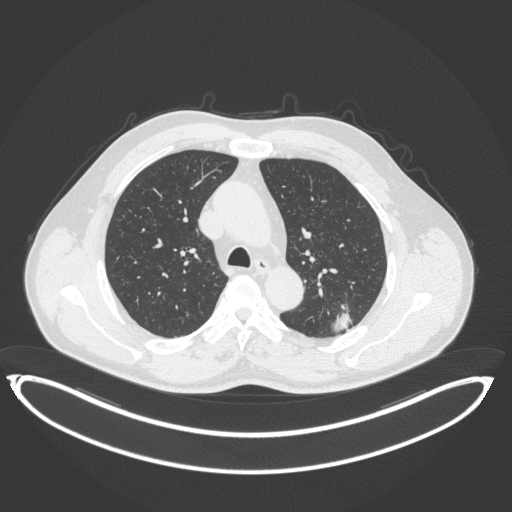
Chest CT, one axial slice. Position 251 of 399 along the scan axis. Reconstruction kernel B31f. 120 kVp. Lung window (W 1500 / L -600 HU). 1 mm slice thickness. 512 × 512 image matrix. Male patient, age 58 years. From the clinical record (not read from this slice): clinical TNM (as recorded): T1c N0 M0; histopathological grade: G1-2.
Outlined on this slice (bounding box drawn by a radiologist):
- lung tumour (recorded histology: adenocarcinoma): bounding box [x1, y1, x2, y2] px = [326, 303, 357, 334]